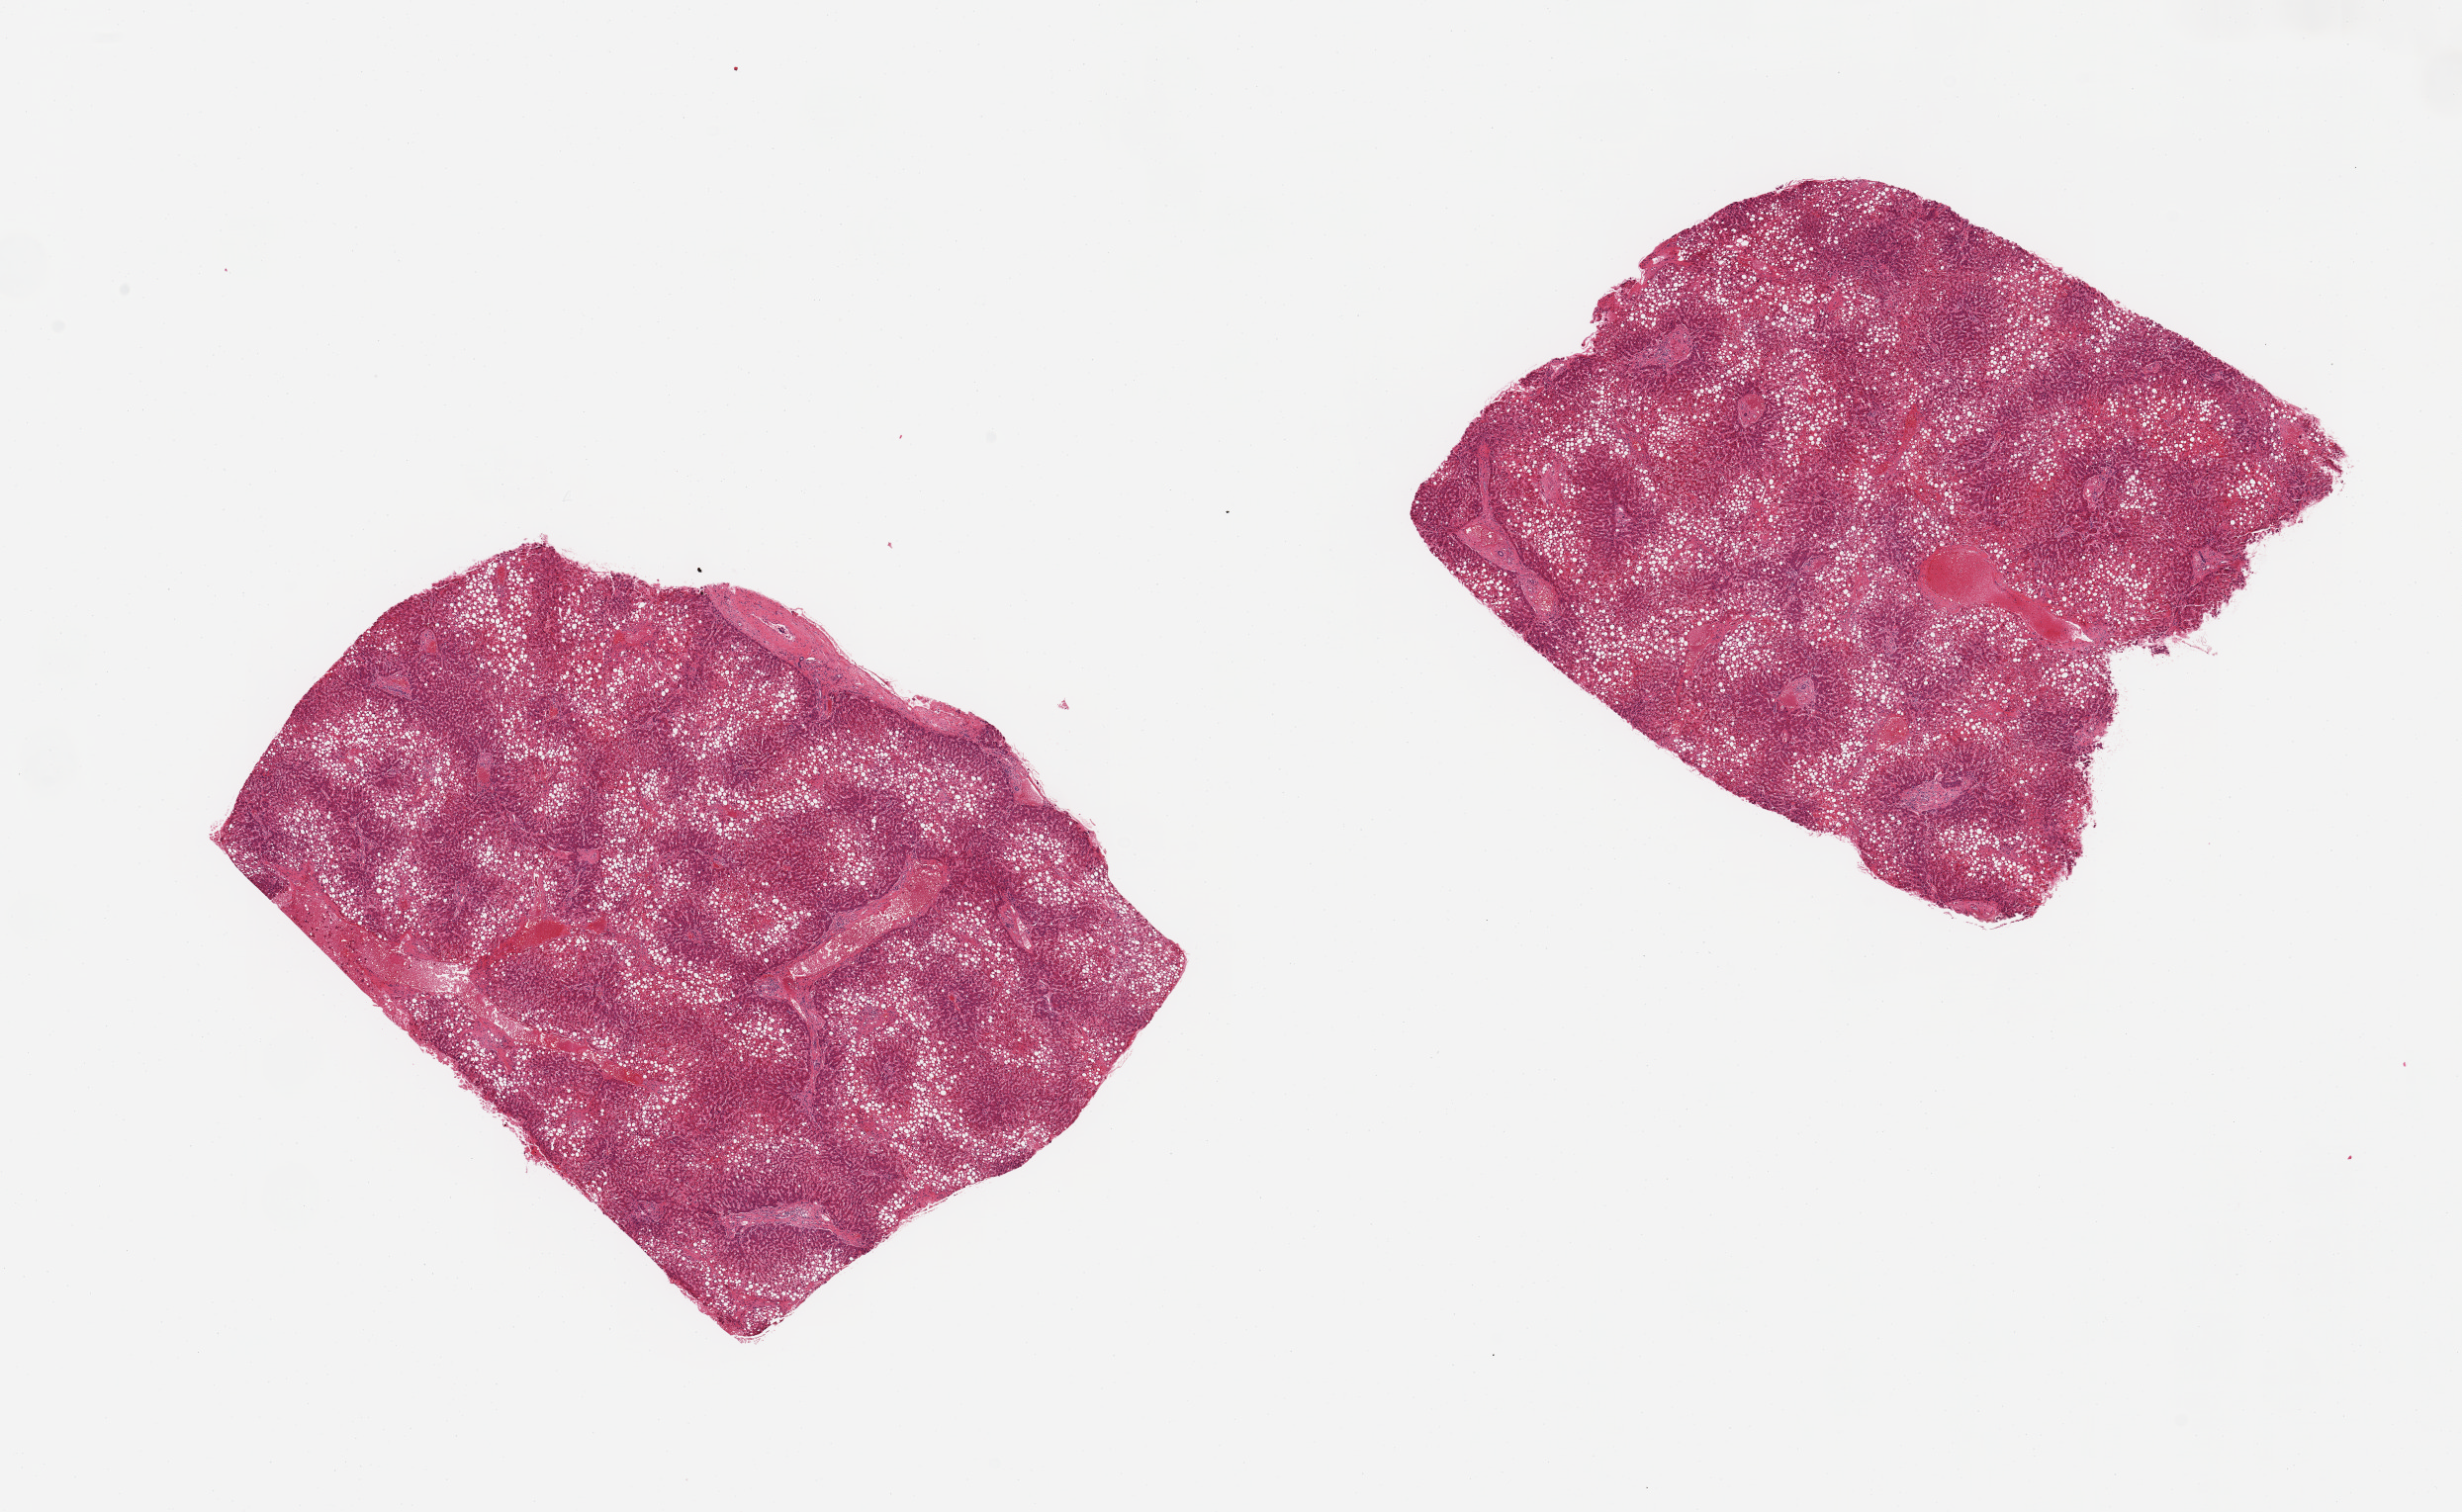
Haematoxylin and eosin whole-slide image, whole scanned area (about 19.7 x 12.1 mm) shown as a low-resolution overview, PAXgene-fixed paraffin-embedded (PFPE) section, section of liver (target tissue), tissue donor sample.
* reviewer comment on this tissue sample: 2 pieces, diffuse macrovesicular steatosis involves ~60% of parenchyma; moderate passive congestion